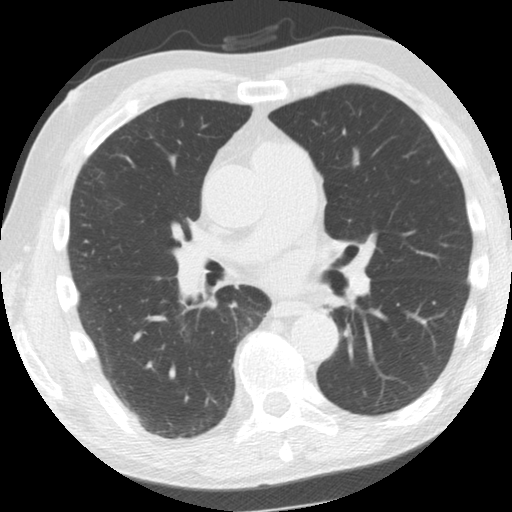
Chest CT (low-dose screening protocol), one axial image, second annual screen, lung window (W 1500 / L -600 HU), slice 75 of 156 in the series. Male participant, aged 61 years at enrolment. Former smoker at enrolment.
Lesion marked by an expert reader, bounding box (x1, y1, x2, y2) in pixels: (299, 291, 347, 329). No non-calcified nodule or mass ≥4 mm was recorded by the screening reader at this exam. Official screen result: negative screen, minor abnormalities not suspicious for lung cancer.